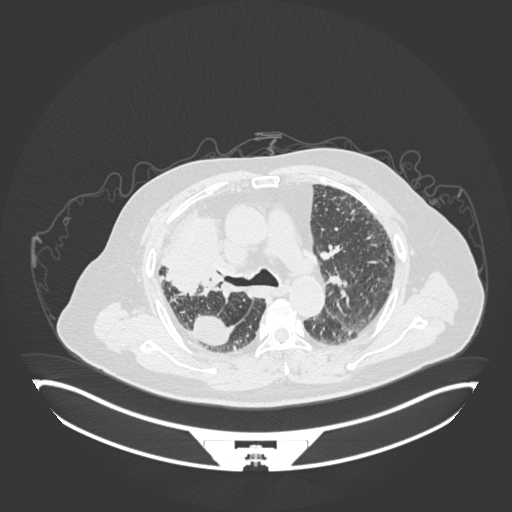
Chest CT, one axial slice. 120 kVp. Lung window (W 1500 / L -600 HU). 1 mm slice thickness. 512 × 512 image matrix. Male patient, age 69 years. Case-level facts recorded for this patient, not image findings: clinical TNM (as recorded): T4 N3 M1.
Outlined on this slice (bounding box drawn by a radiologist):
- lung tumour (recorded histology: adenocarcinoma): bounding box (x1, y1, x2, y2) in pixels: (162, 211, 233, 300)